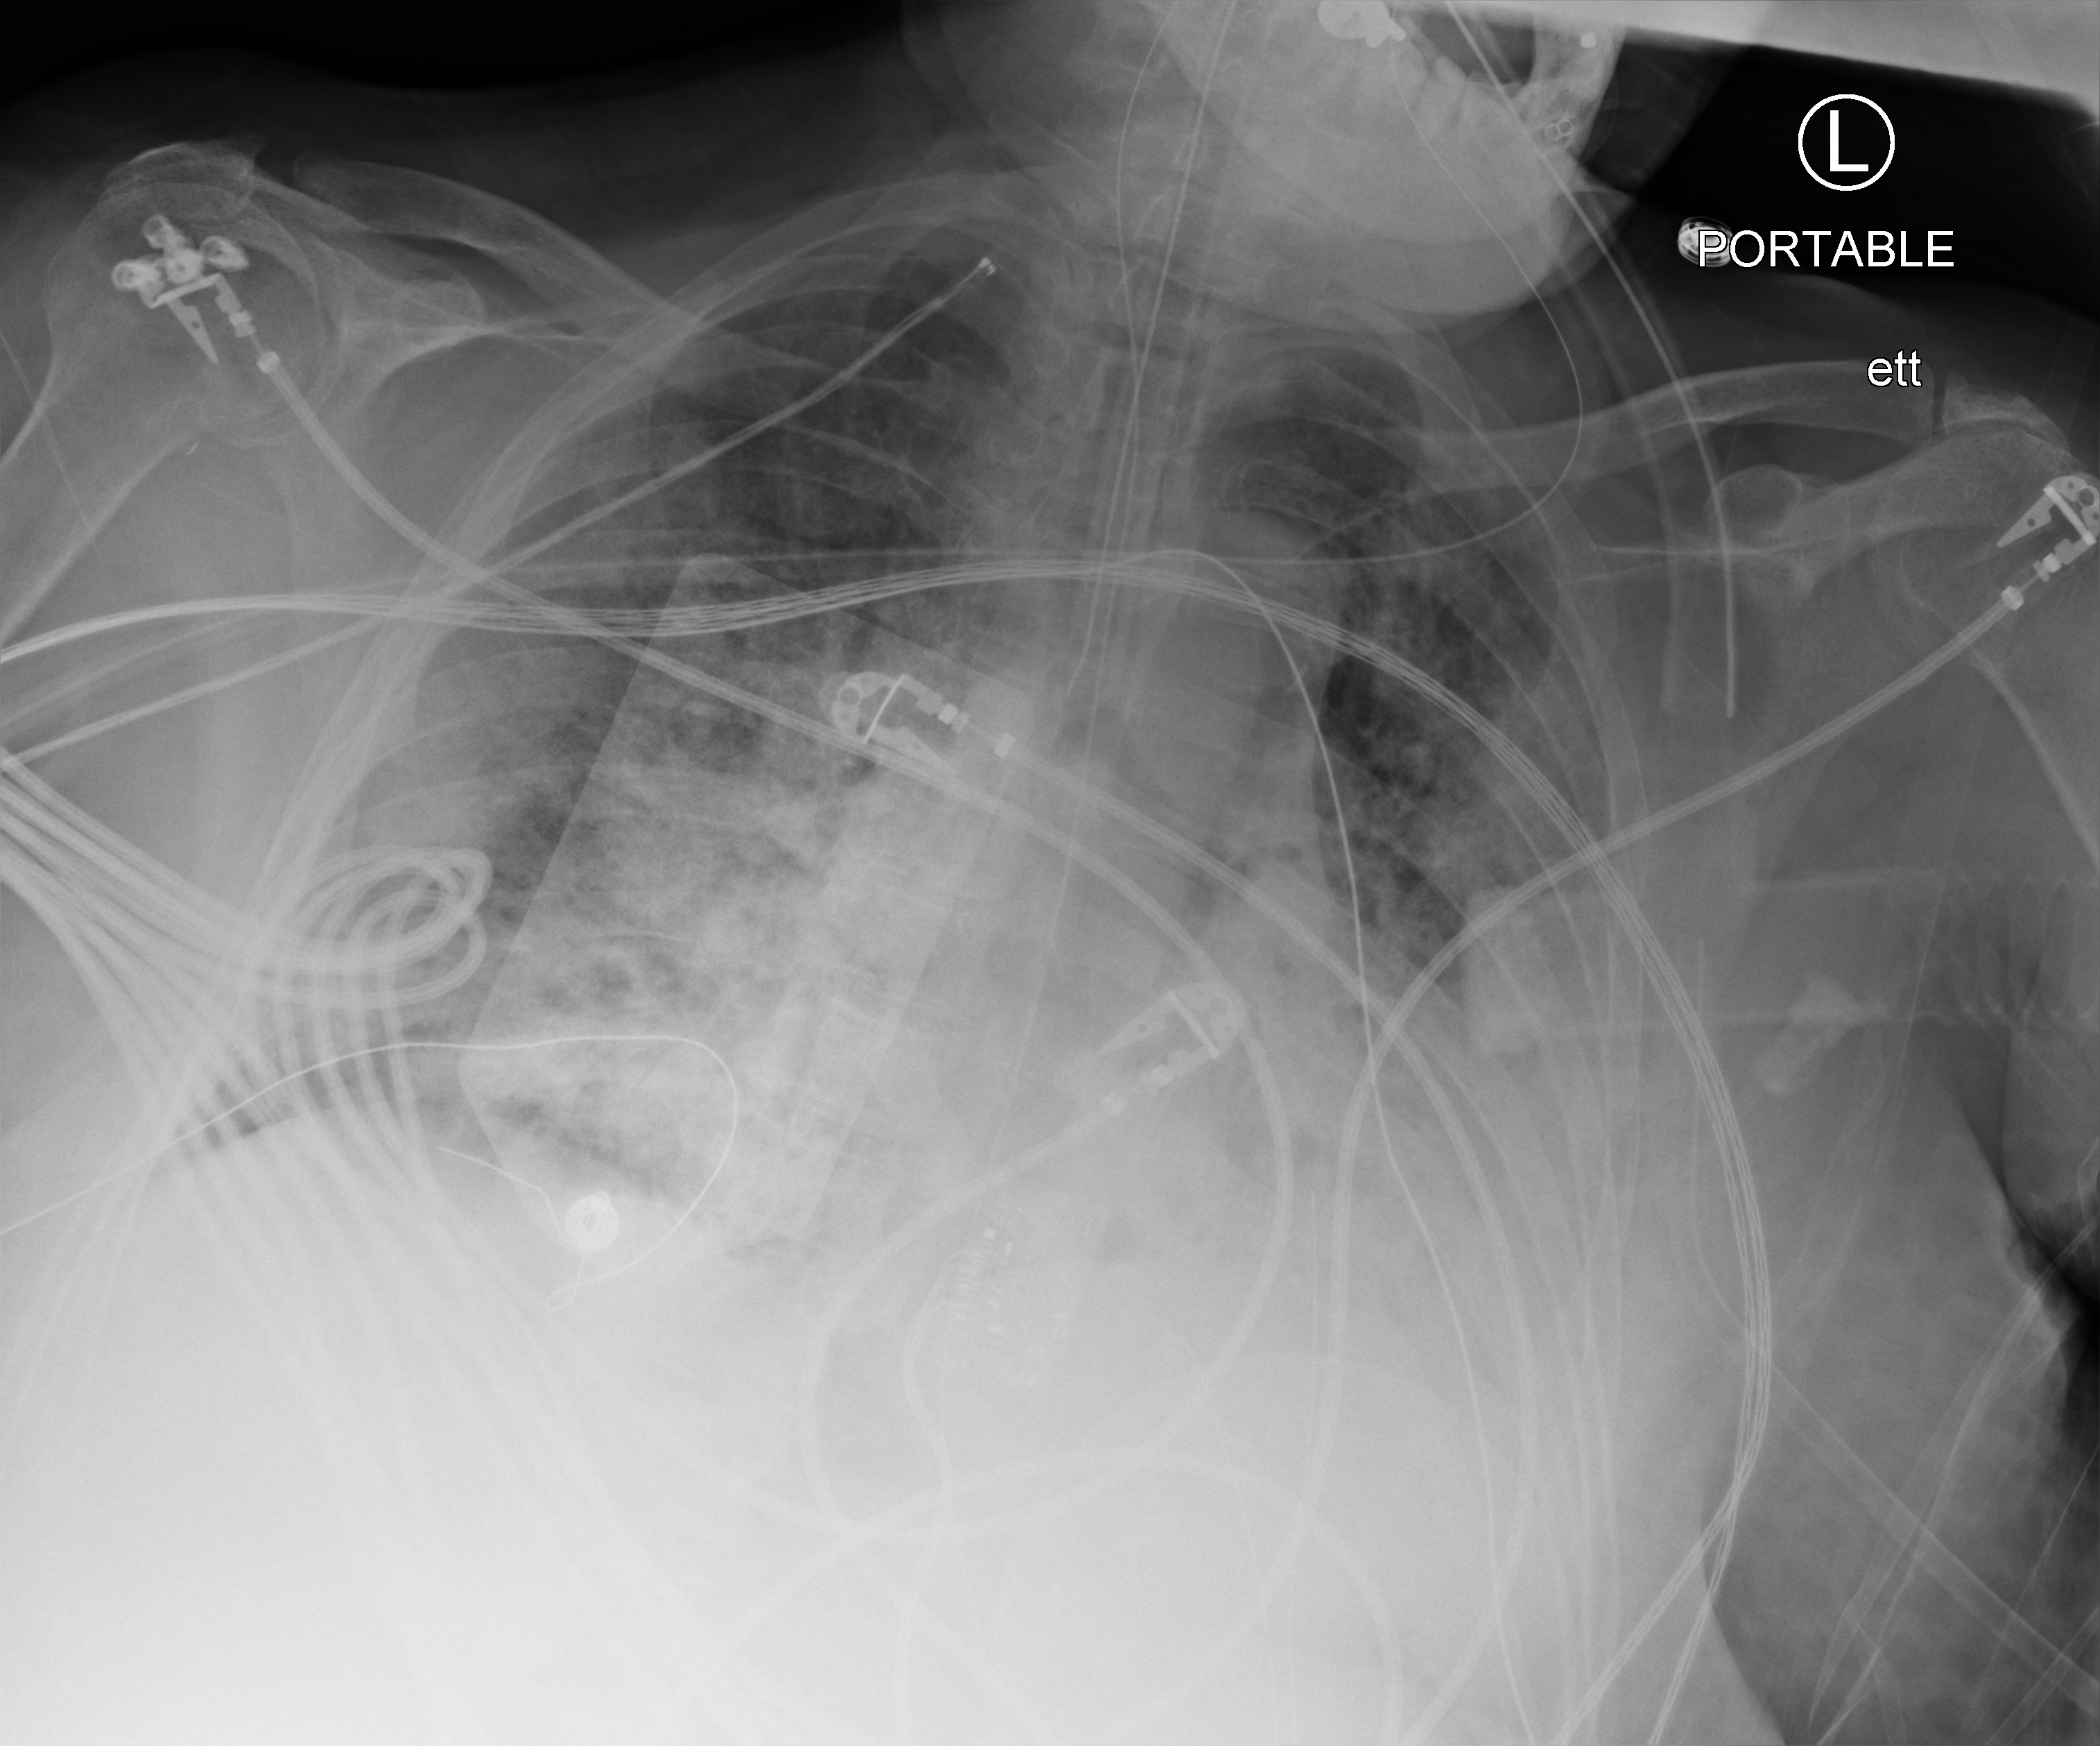
Chest X-ray (portable); anteroposterior (AP) projection. Female patient hospitalised with COVID-19, age 60–74 years.
From the hospital-stay record, not from the radiograph (when in the stay this image was taken is not recorded): hypertension (admission record): yes; chronic kidney disease (admission record): no.